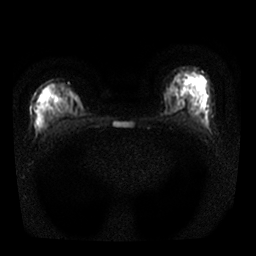
Breast MRI, one axial slice. Slice 9 of 25 in the series (ordered by position). Diffusion-weighted series; image 2 of 4 stored at this slice position (different b-values; order by instance number). 1.5 T. 4 mm slice thickness. 256 × 256 image matrix. Female patient.
Annotated regions visible in this slice (manually delineated by an expert):
- tumour on diffusion-weighted imaging: bounding box <197,111,203,117> (left, top, right, bottom; pixels)